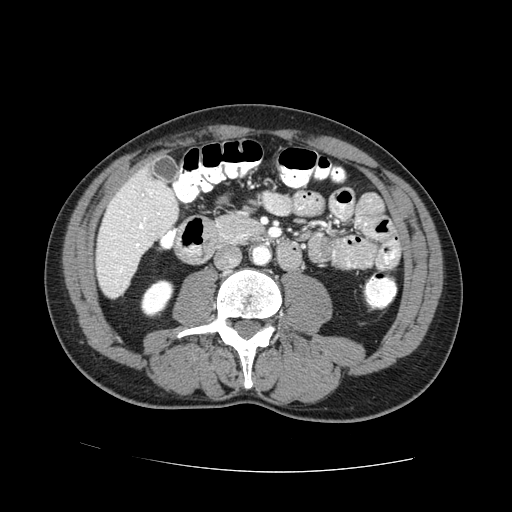
Contrast-enhanced abdominal CT (liver protocol), one axial slice; slice 15 of 73 in the series (ordered by position); reconstruction kernel STANDARD; 100 kVp; one of 2 acquisitions stored at this slice position; soft-tissue window (W 400 / L 40 HU); 2.5 mm slice thickness; 512 × 512 image matrix, field of view 380 × 380 mm. Case-level facts recorded for this patient, not image findings: diagnosis: hepatocellular carcinoma (patient treated with transarterial chemoembolisation; whether this scan precedes or follows treatment is not stated here); TNM stage (as recorded): Stage-IVA; Child-Pugh class: A; tumour differentiation: no biopsy; tumour nodularity: uninodular.
Structures marked on this image (semi-automatically segmented with operator editing):
- liver parenchyma outside the tumour (the mass and vessels are separate outlines, so this box may not span the whole liver): bounding box (x1, y1, x2, y2) in pixels: (96, 162, 178, 298)
- liver vessels: (121, 213, 159, 270)